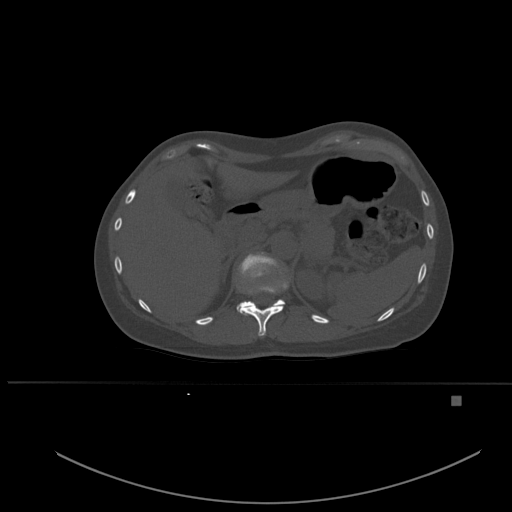
CT including the spine, one axial slice; bone window (W 1800 / L 400 HU); 1.5 mm slice thickness; 512 × 512 image matrix, field of view 443 × 443 mm. Female patient, age 49 years. From the clinical record (not read from this slice): primary cancer: breast.
Annotated regions visible in this slice (semi-automatic segmentation, software-assisted and operator-edited):
- T11 vertebra: bounding box (x1, y1, x2, y2) in pixels: (237, 272, 288, 336)
- T12 vertebra: (236, 253, 285, 309)